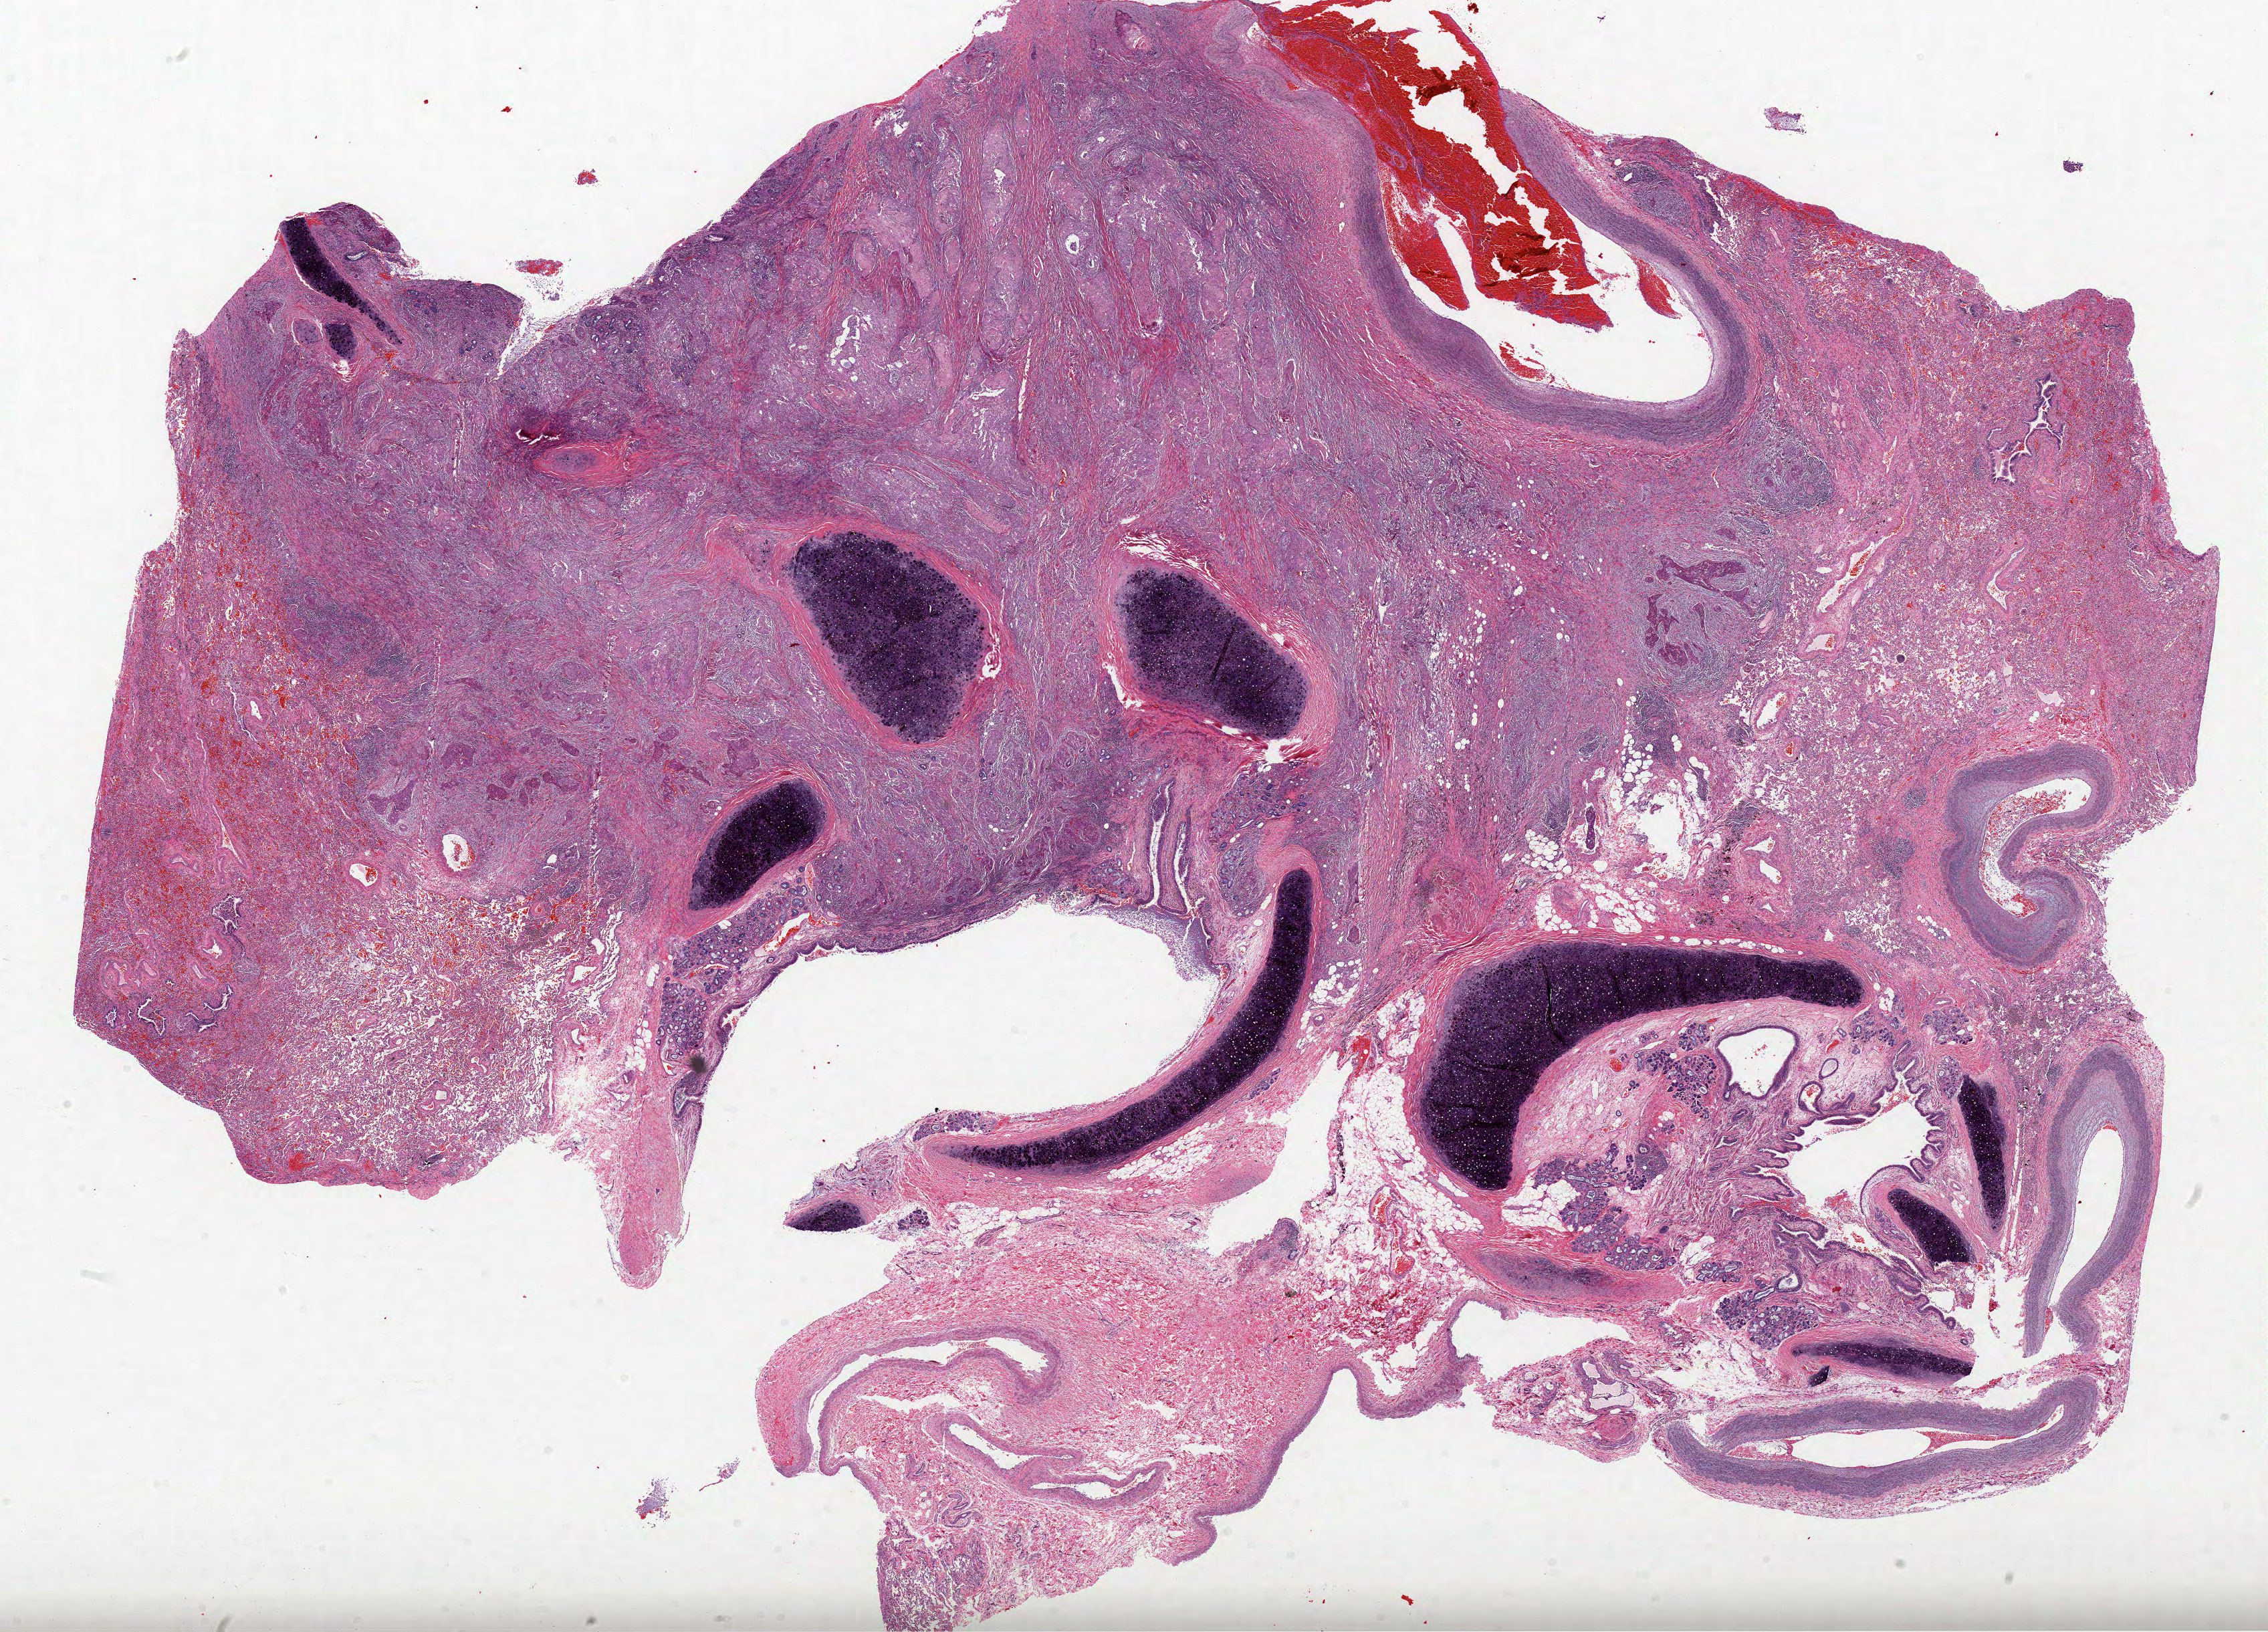
Digitized H&E-stained tissue section (whole slide), low-resolution overview of the scanned area, about 27.4 x 19.7 mm, formalin-fixed paraffin-embedded (FFPE) diagnostic section, primary tumour sample from the lung. Female, age 65 years at initial diagnosis.
AJCC pathologic stage: IIIA (7th edition). Pathologic diagnosis: Squamous cell carcinoma, NOS.